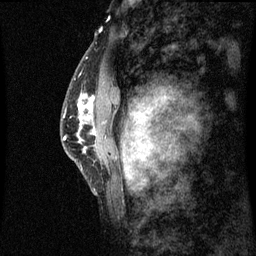
Breast MRI (dynamic contrast-enhanced), one sagittal slice. Position 43 of 60 along the scan axis. Dynamic contrast-enhanced series, image 2 of 3 at this slice position (ordered by acquisition). 1.5 T. TE 4.2 ms, TR 8.9 ms. 2 mm slice thickness. 256 × 256 image matrix, field of view 200 × 200 mm. Patient: female, 50 years. From the clinical record (not read from this slice): setting: breast cancer imaged before/during neoadjuvant chemotherapy; receptor status: triple-negative.
Annotated regions visible in this slice (semi-automatically segmented with operator editing):
- analysis volume of interest (the breast-tissue region the enhancement analysis was run in; not a lesion): bounding box (x1, y1, x2, y2) in pixels: (68, 80, 98, 169)
- tumour enhancement mask (voxels above the 70 % enhancement threshold inside the analysis volume of interest): (81, 100, 96, 135)